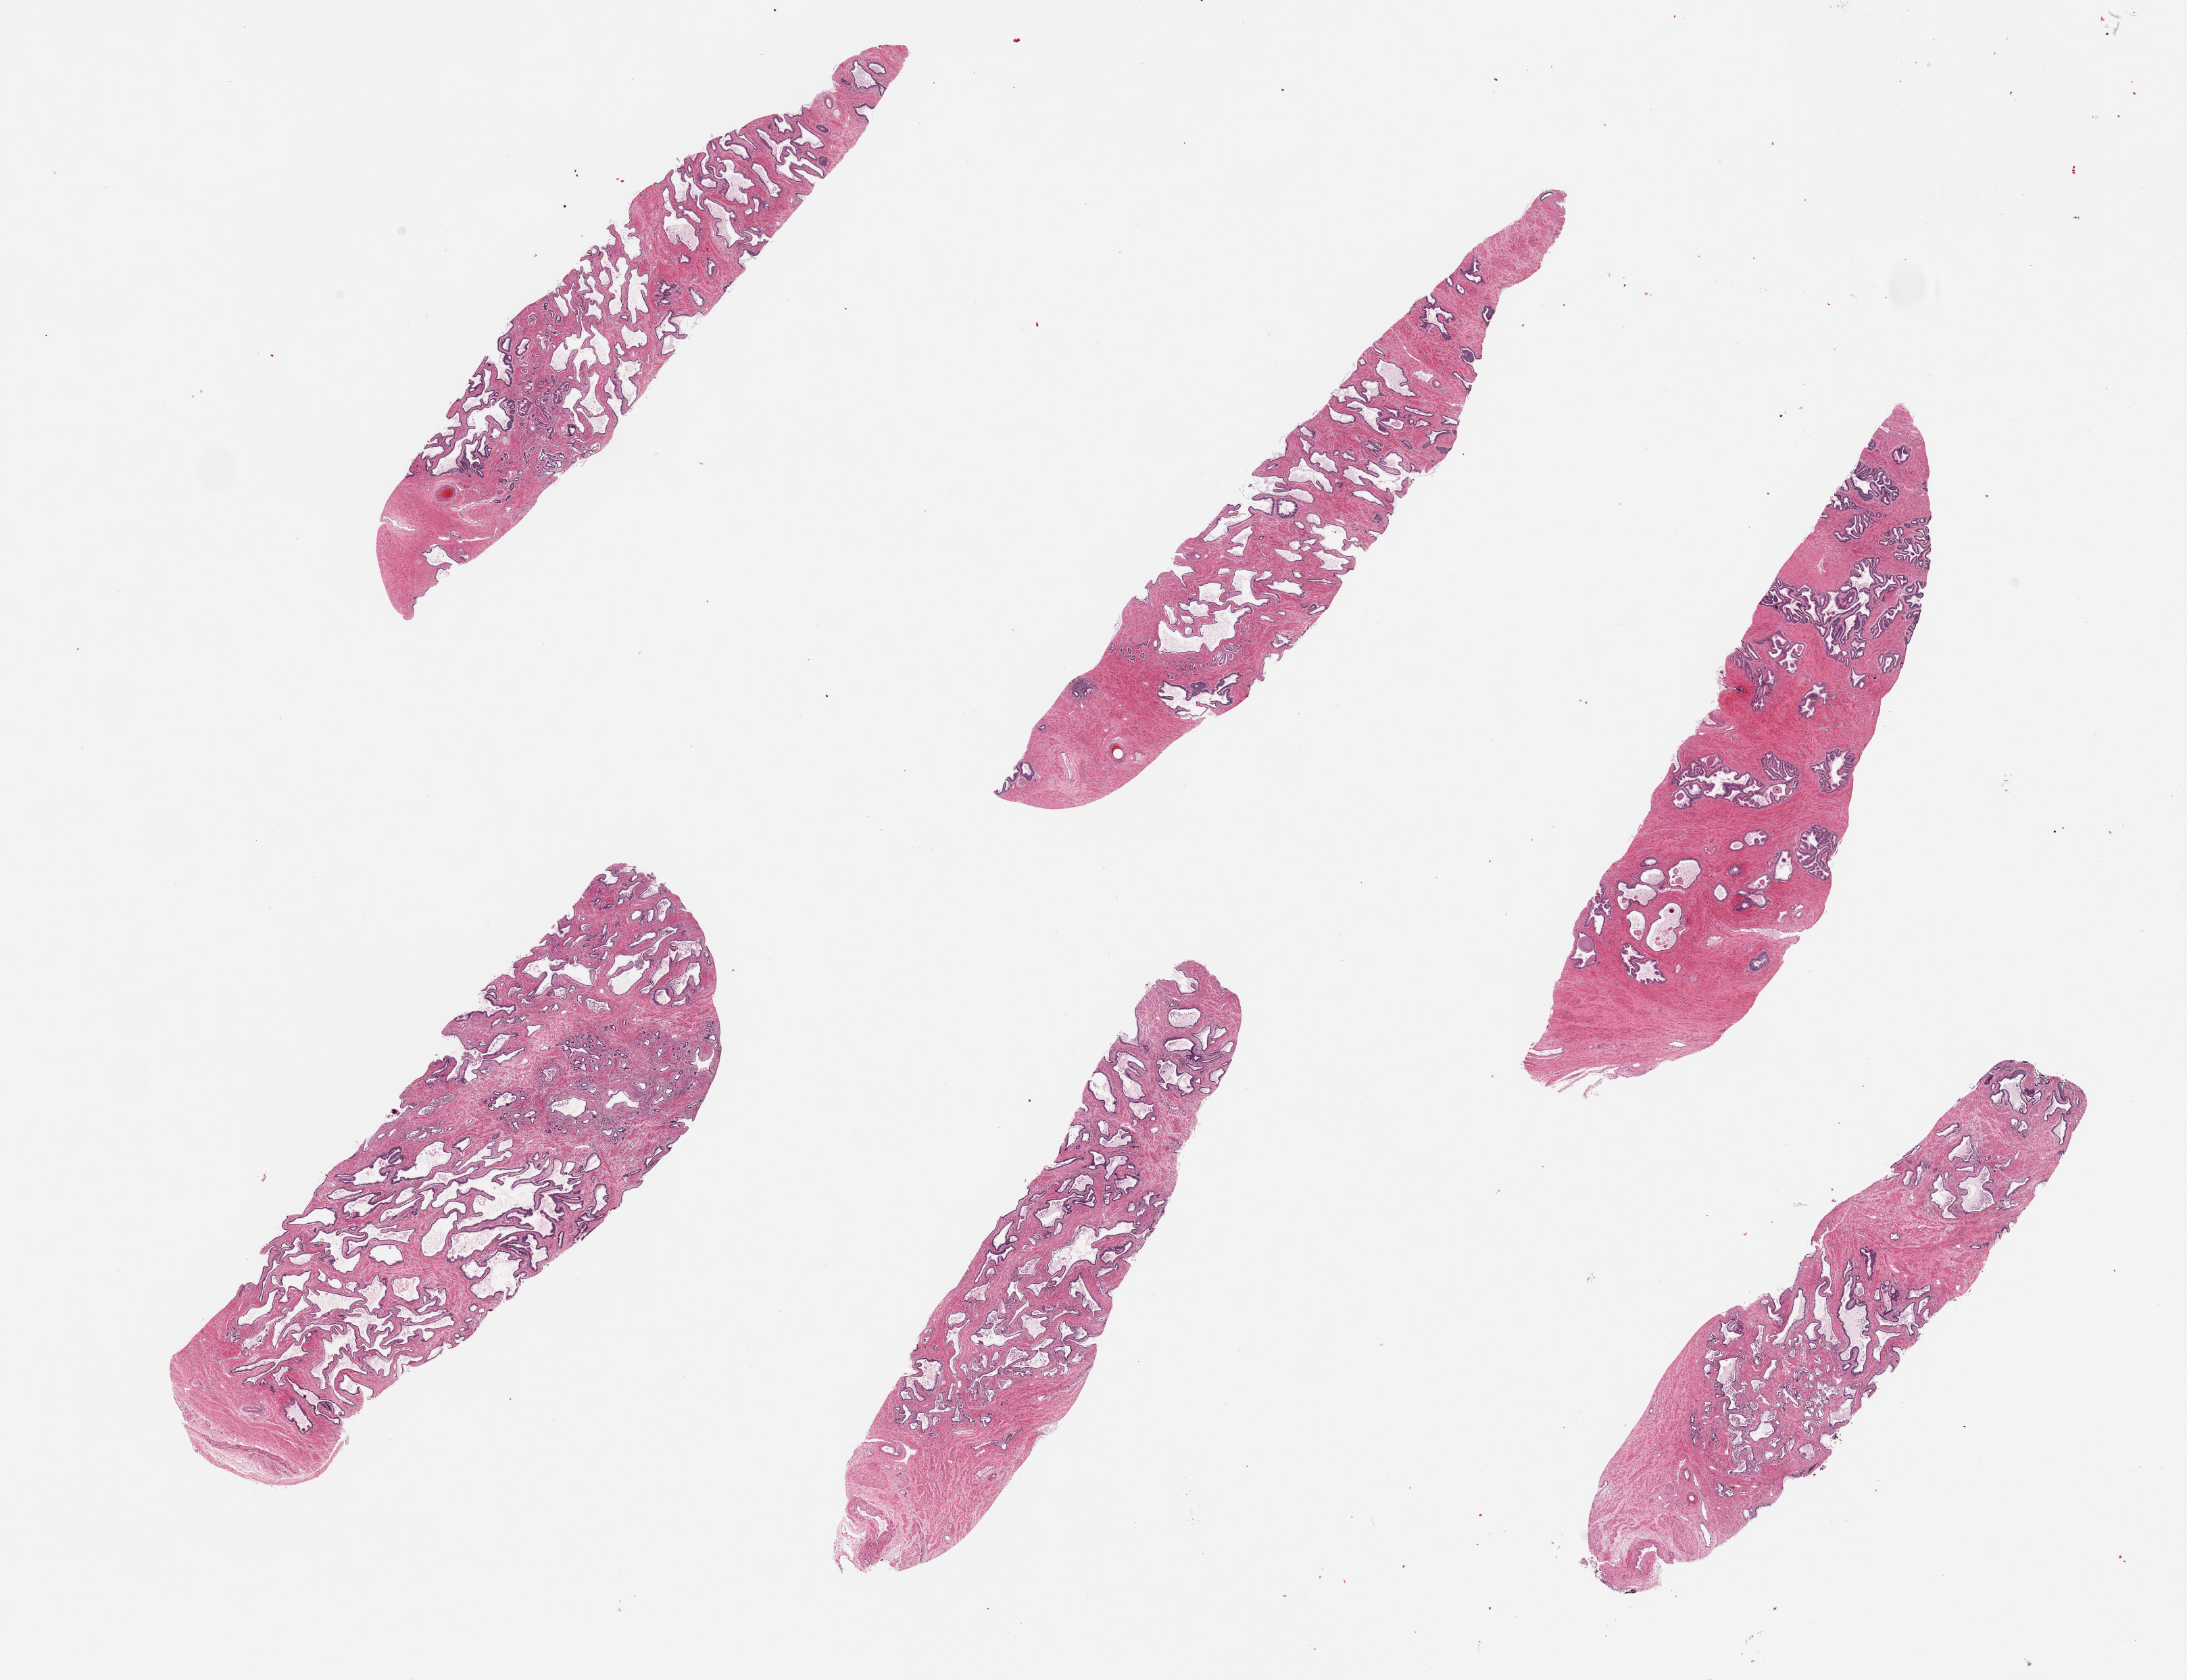
Digitized haematoxylin and eosin-stained section, low-resolution overview of the scanned area, about 25.6 x 19.7 mm. PAXgene-fixed paraffin-embedded (PFPE) section. Section of prostate (target tissue). Donor tissue sample. Male donor.
Pathologist's review note for this sample: 6 pieces. Prostate not colon.